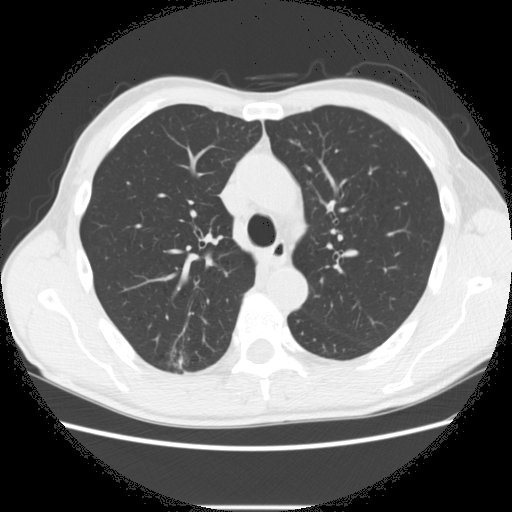
Axial slice from a low-dose chest CT screening exam, second annual screen, lung window (W 1500 / L -600 HU), 2.5 mm slice thickness, standard (soft-tissue) reconstruction kernel (STANDARD), 120 kVp, slice 87 of 282 in the series, 512 × 512 image matrix. Male participant, aged 66 years at enrolment.
- Expert-annotated lung lesion, bounding box [x1, y1, x2, y2] px = [164, 343, 219, 384].
- The screening reader recorded 5 non-calcified nodules or masses ≥4 mm on this exam (right lower lobe, right upper lobe, right upper lobe, right upper lobe, left lower lobe); which of them this box marks is not recorded.